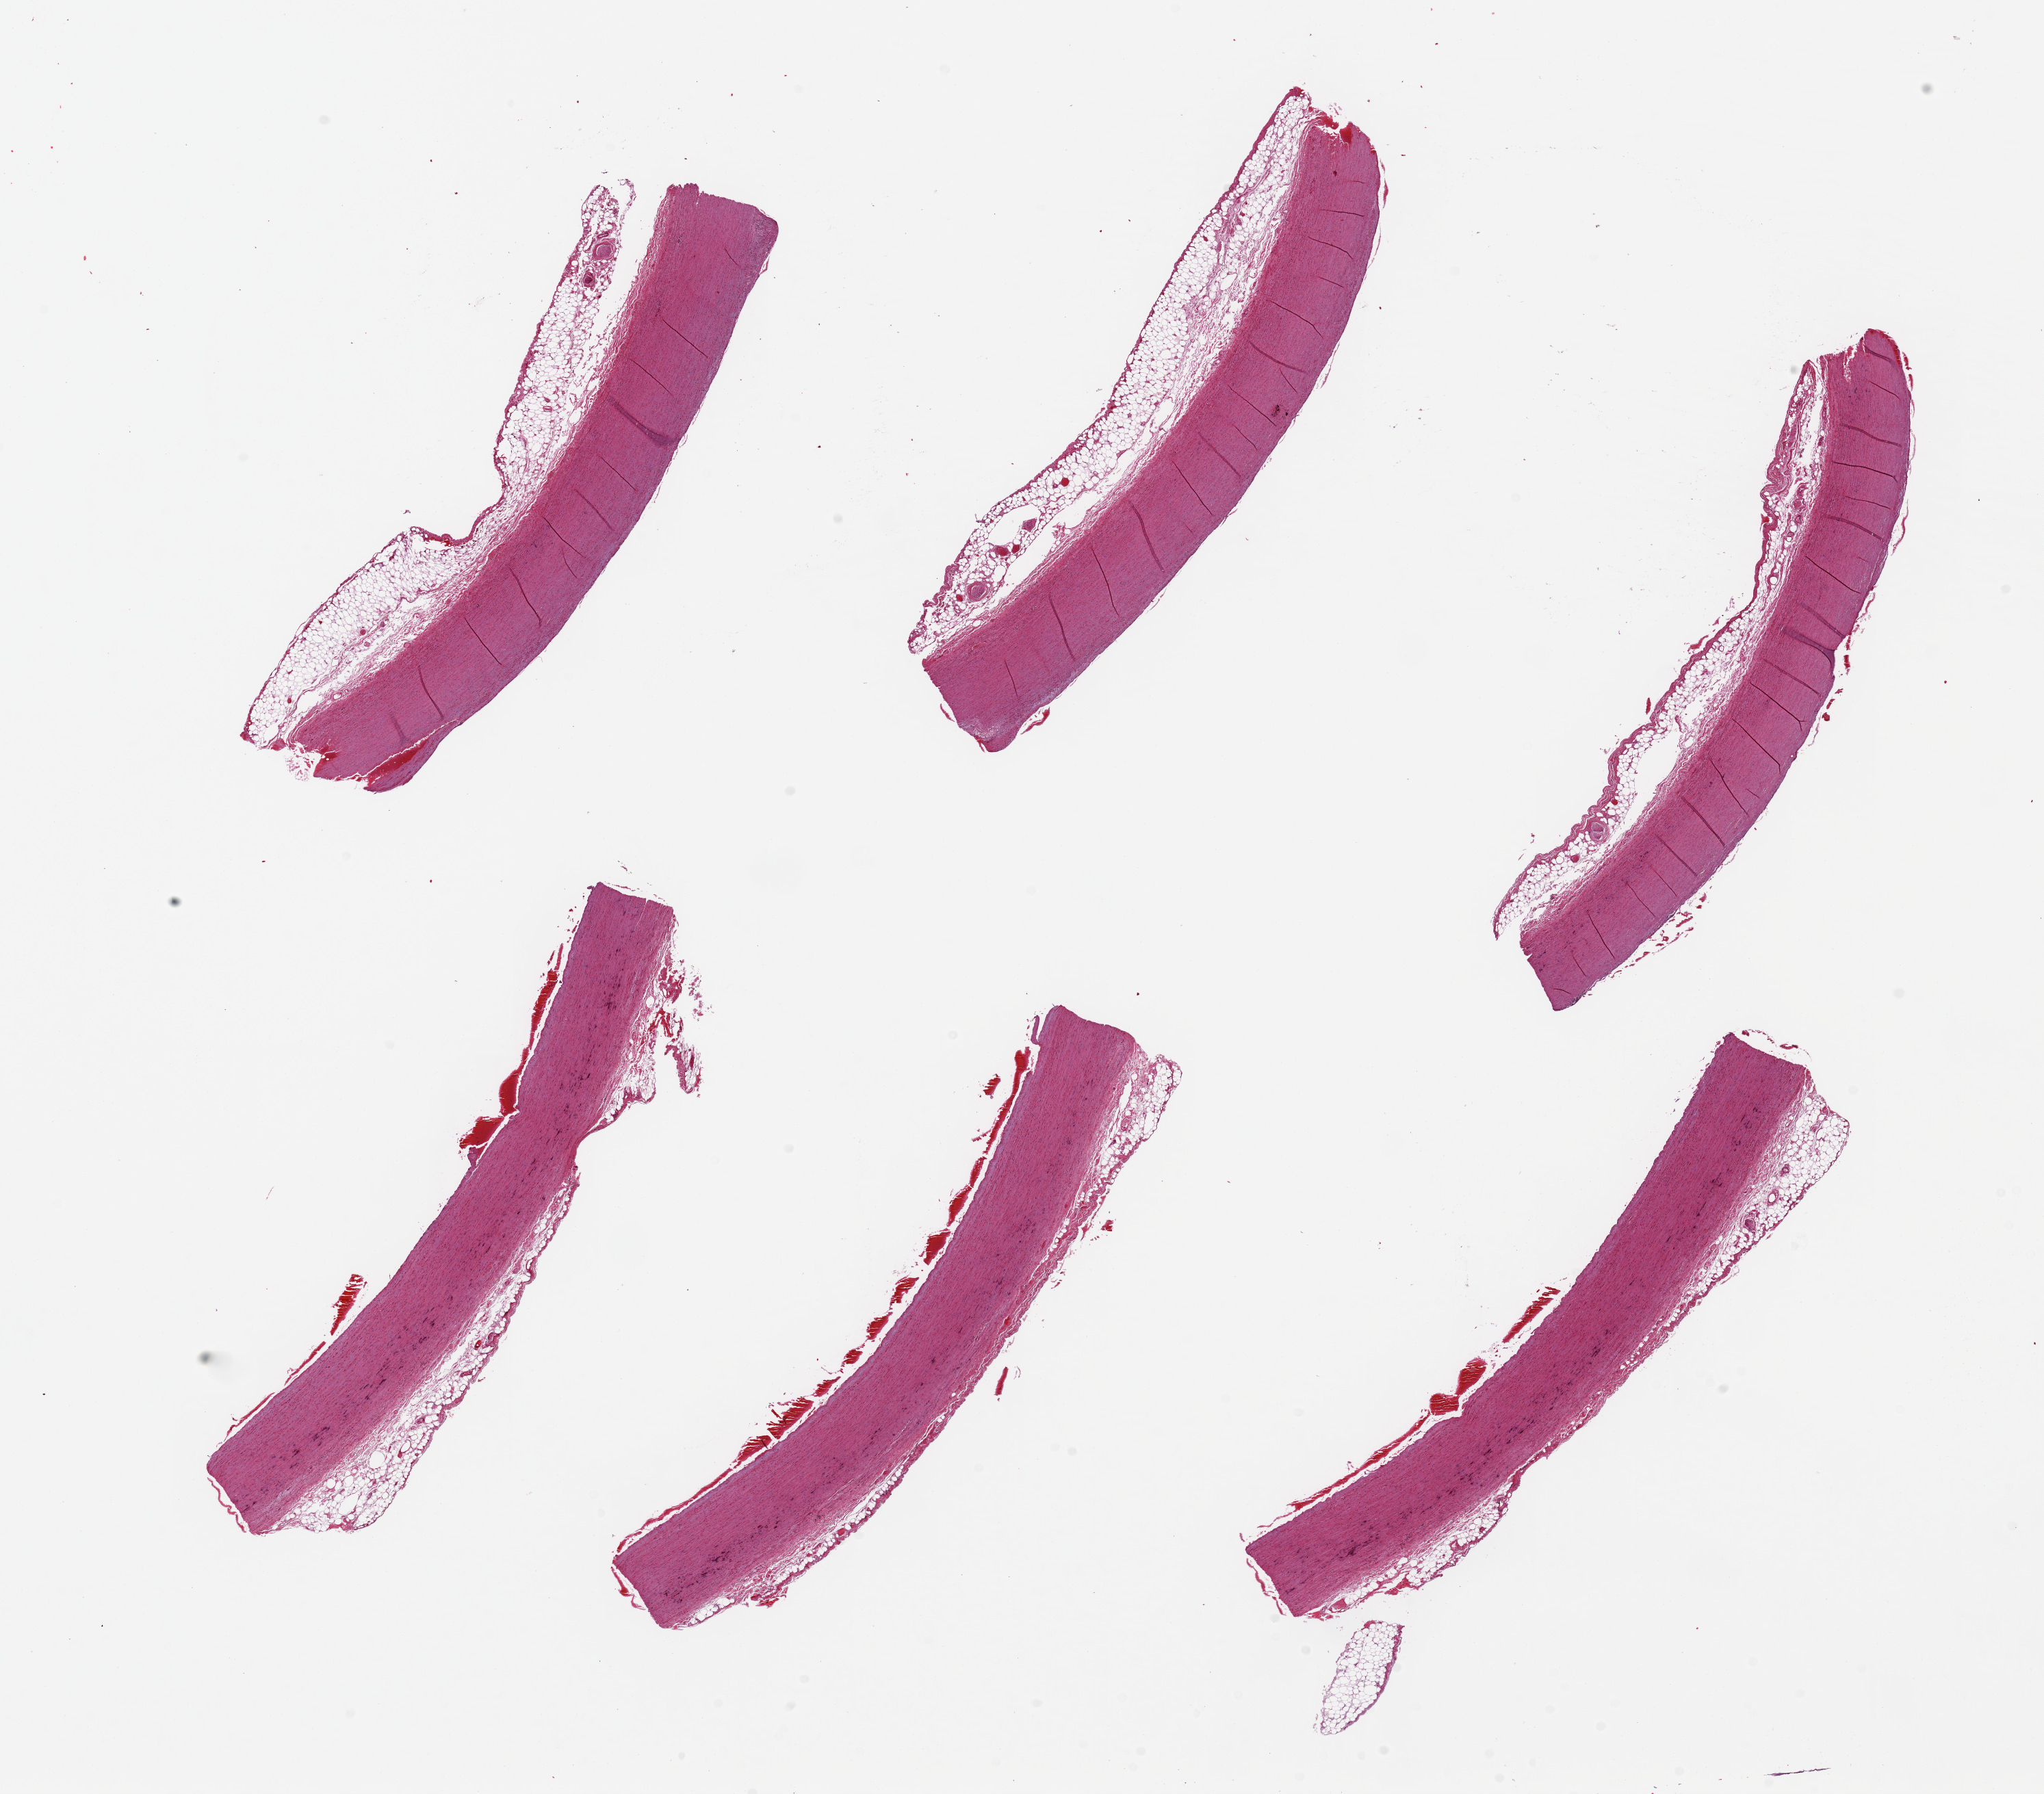
Digitized haematoxylin and eosin-stained section, shown as a low-resolution overview of the whole scanned area (about 23.6 x 20.7 mm); PAXgene-fixed paraffin-embedded (PFPE) section; sampled site (target tissue): aorta; donor tissue sample. Donor: female.
* pathologist's review note for this sample: 6 pieces, up to 9x1mm; focal calcification, no plaques; up to 1 mm adipose on adventitial side